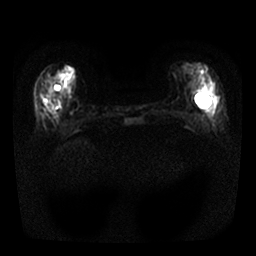
Breast MRI, one axial slice; diffusion-weighted series; image 2 of 4 stored at this slice position (different b-values; order by instance number); 1.5 T; 4 mm slice thickness; 256 × 256 image matrix. Female patient.
Structures marked on this image (expert manual segmentation):
- tumour on diffusion-weighted imaging: bounding box <44,98,48,101> (left, top, right, bottom; pixels)